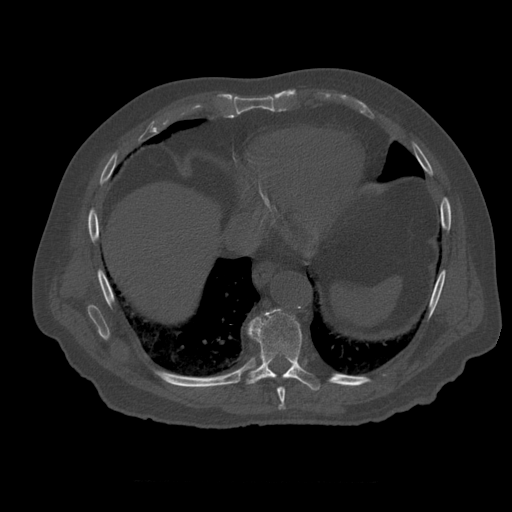
CT including the spine, one axial slice; position 325 of 399 along the scan axis; reconstruction kernel STANDARD; 120 kVp; bone window (W 1800 / L 400 HU); 1.25 mm slice thickness; 512 × 512 image matrix, field of view 407 × 407 mm. Patient age 73 years. Case-level facts recorded for this patient, not image findings: primary cancer: prostate; vertebrae with lytic lesions (as recorded): L2.
Outlined on this slice (semi-automatically segmented with operator editing):
- T8 vertebra: bounding box (x1, y1, x2, y2) in pixels: (278, 387, 286, 410)
- T9 vertebra: (237, 309, 321, 391)